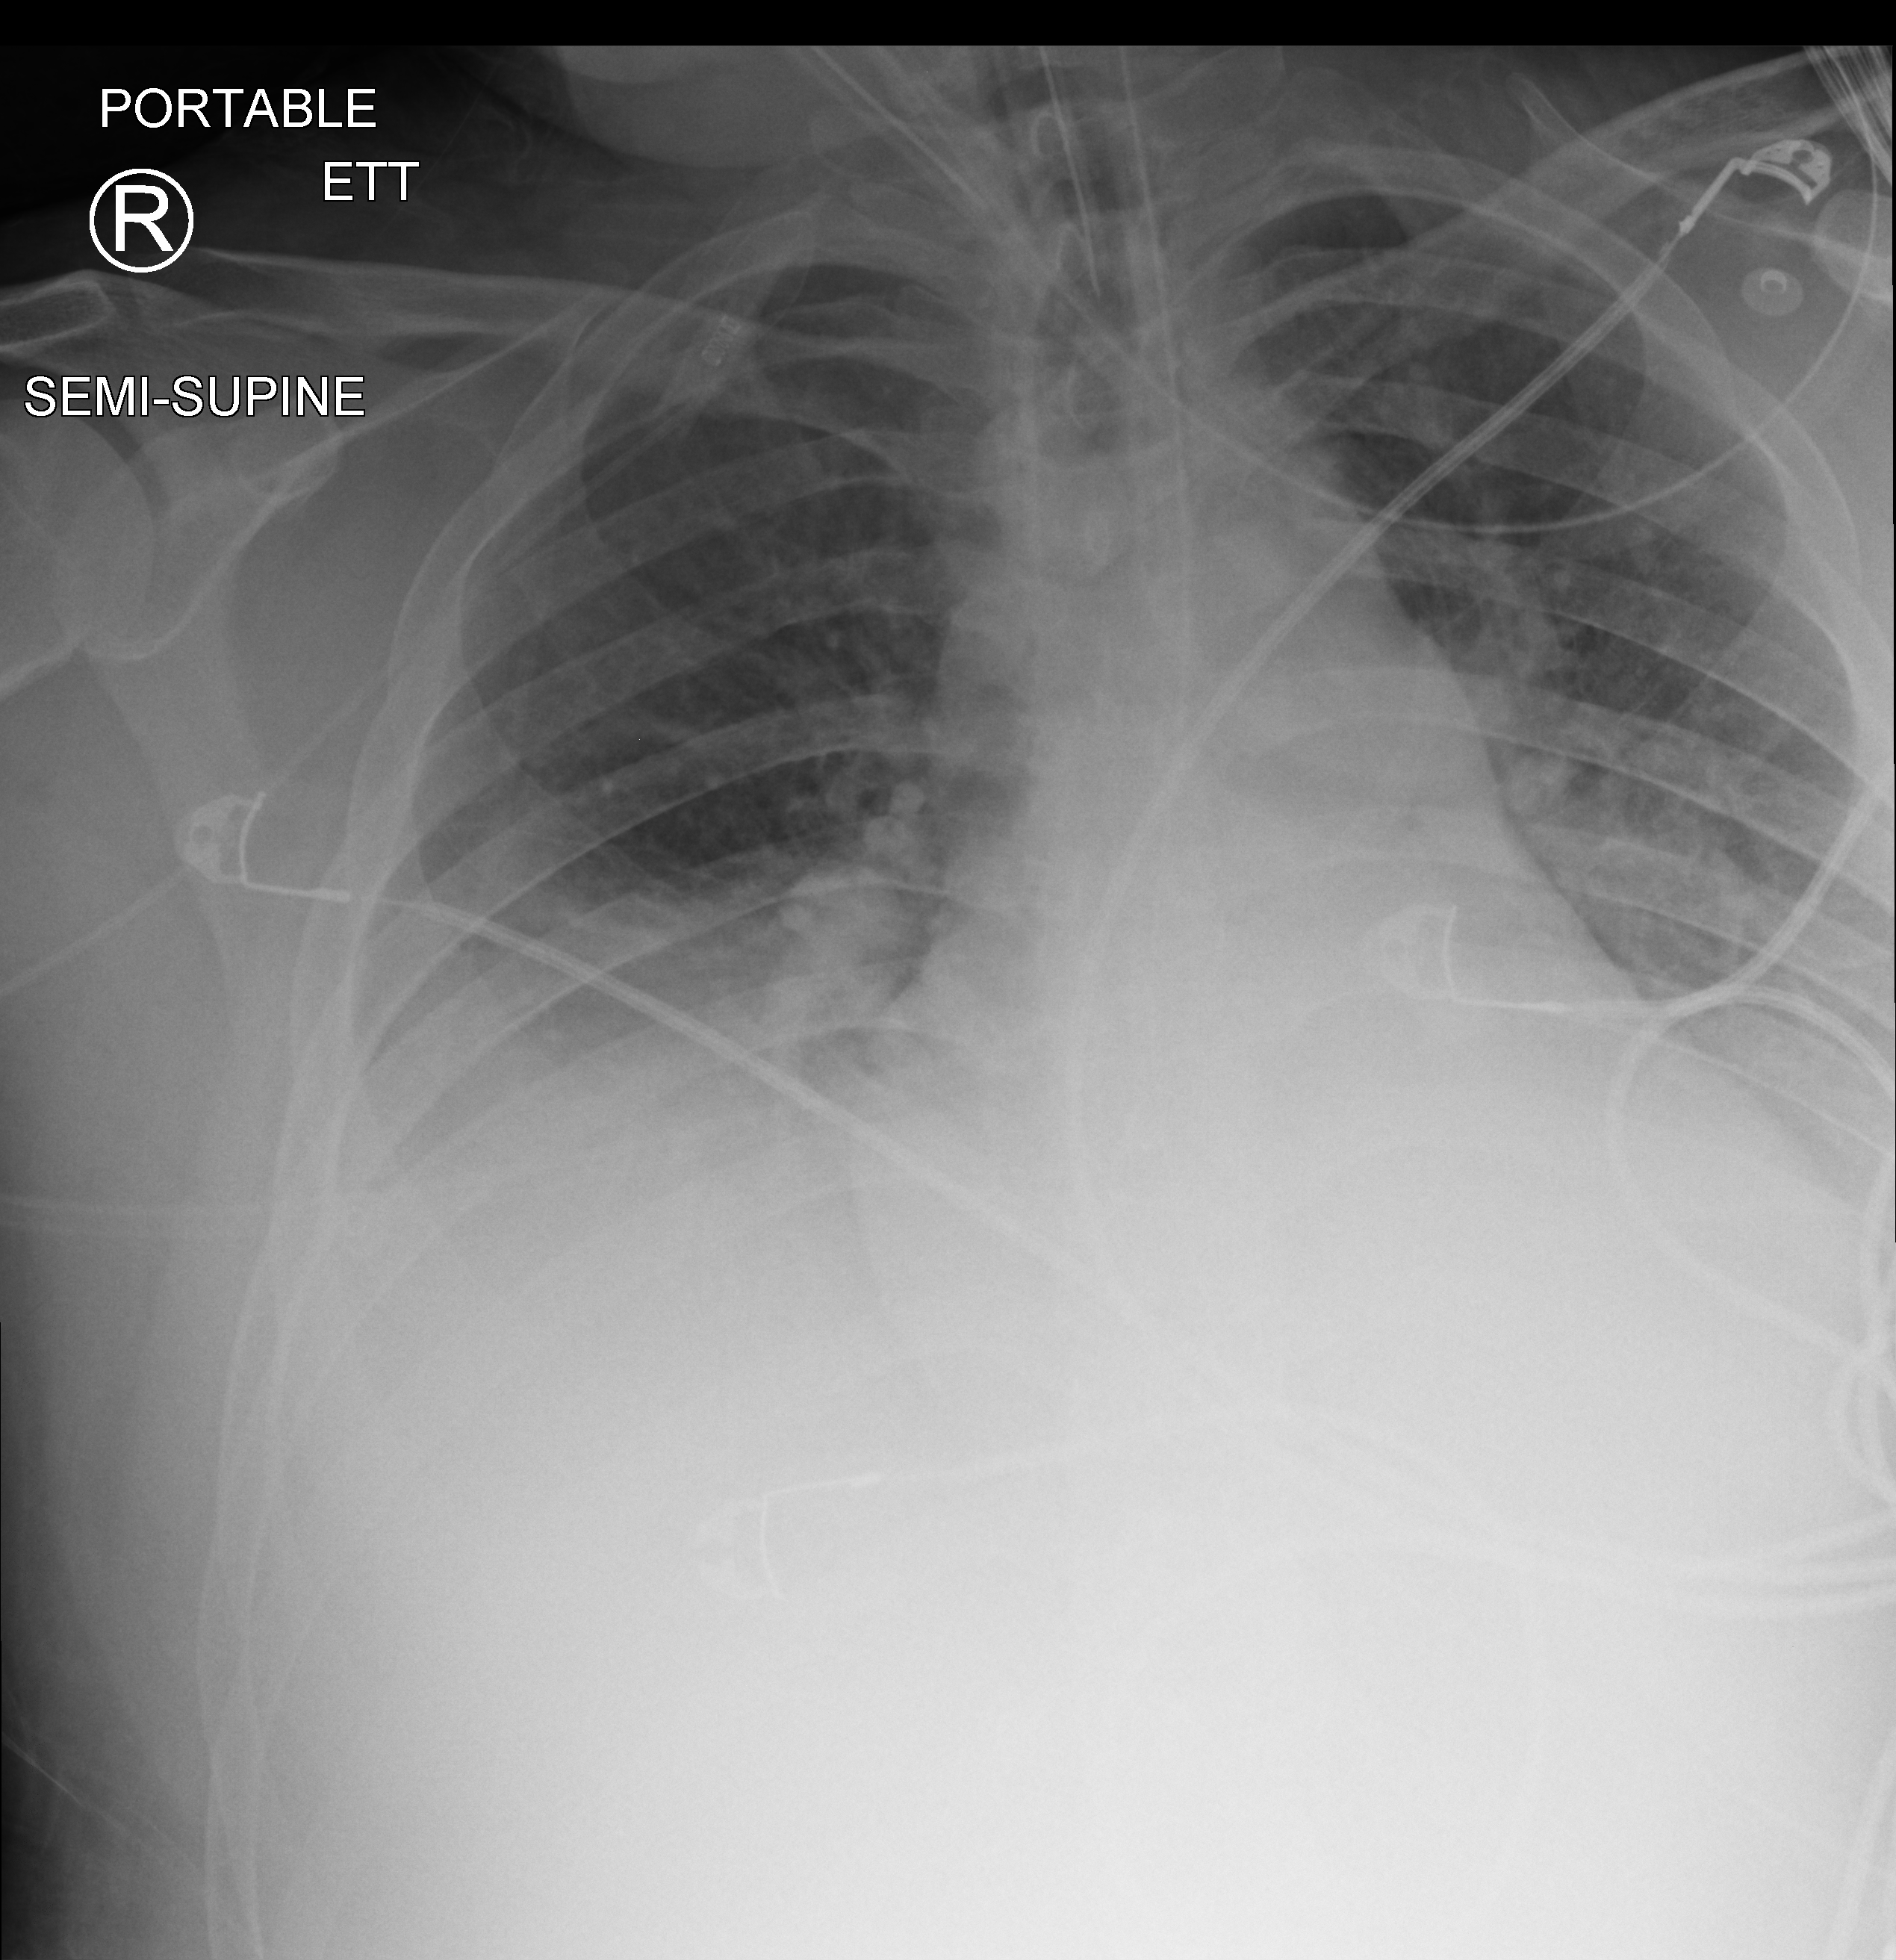
Chest X-ray (portable). Male patient hospitalised with COVID-19, age 18–59 years.
Admission-level facts for this patient (not findings on this image; timing relative to this image not recorded): mechanically ventilated during this hospital stay: yes; length of hospital stay: 61 days.